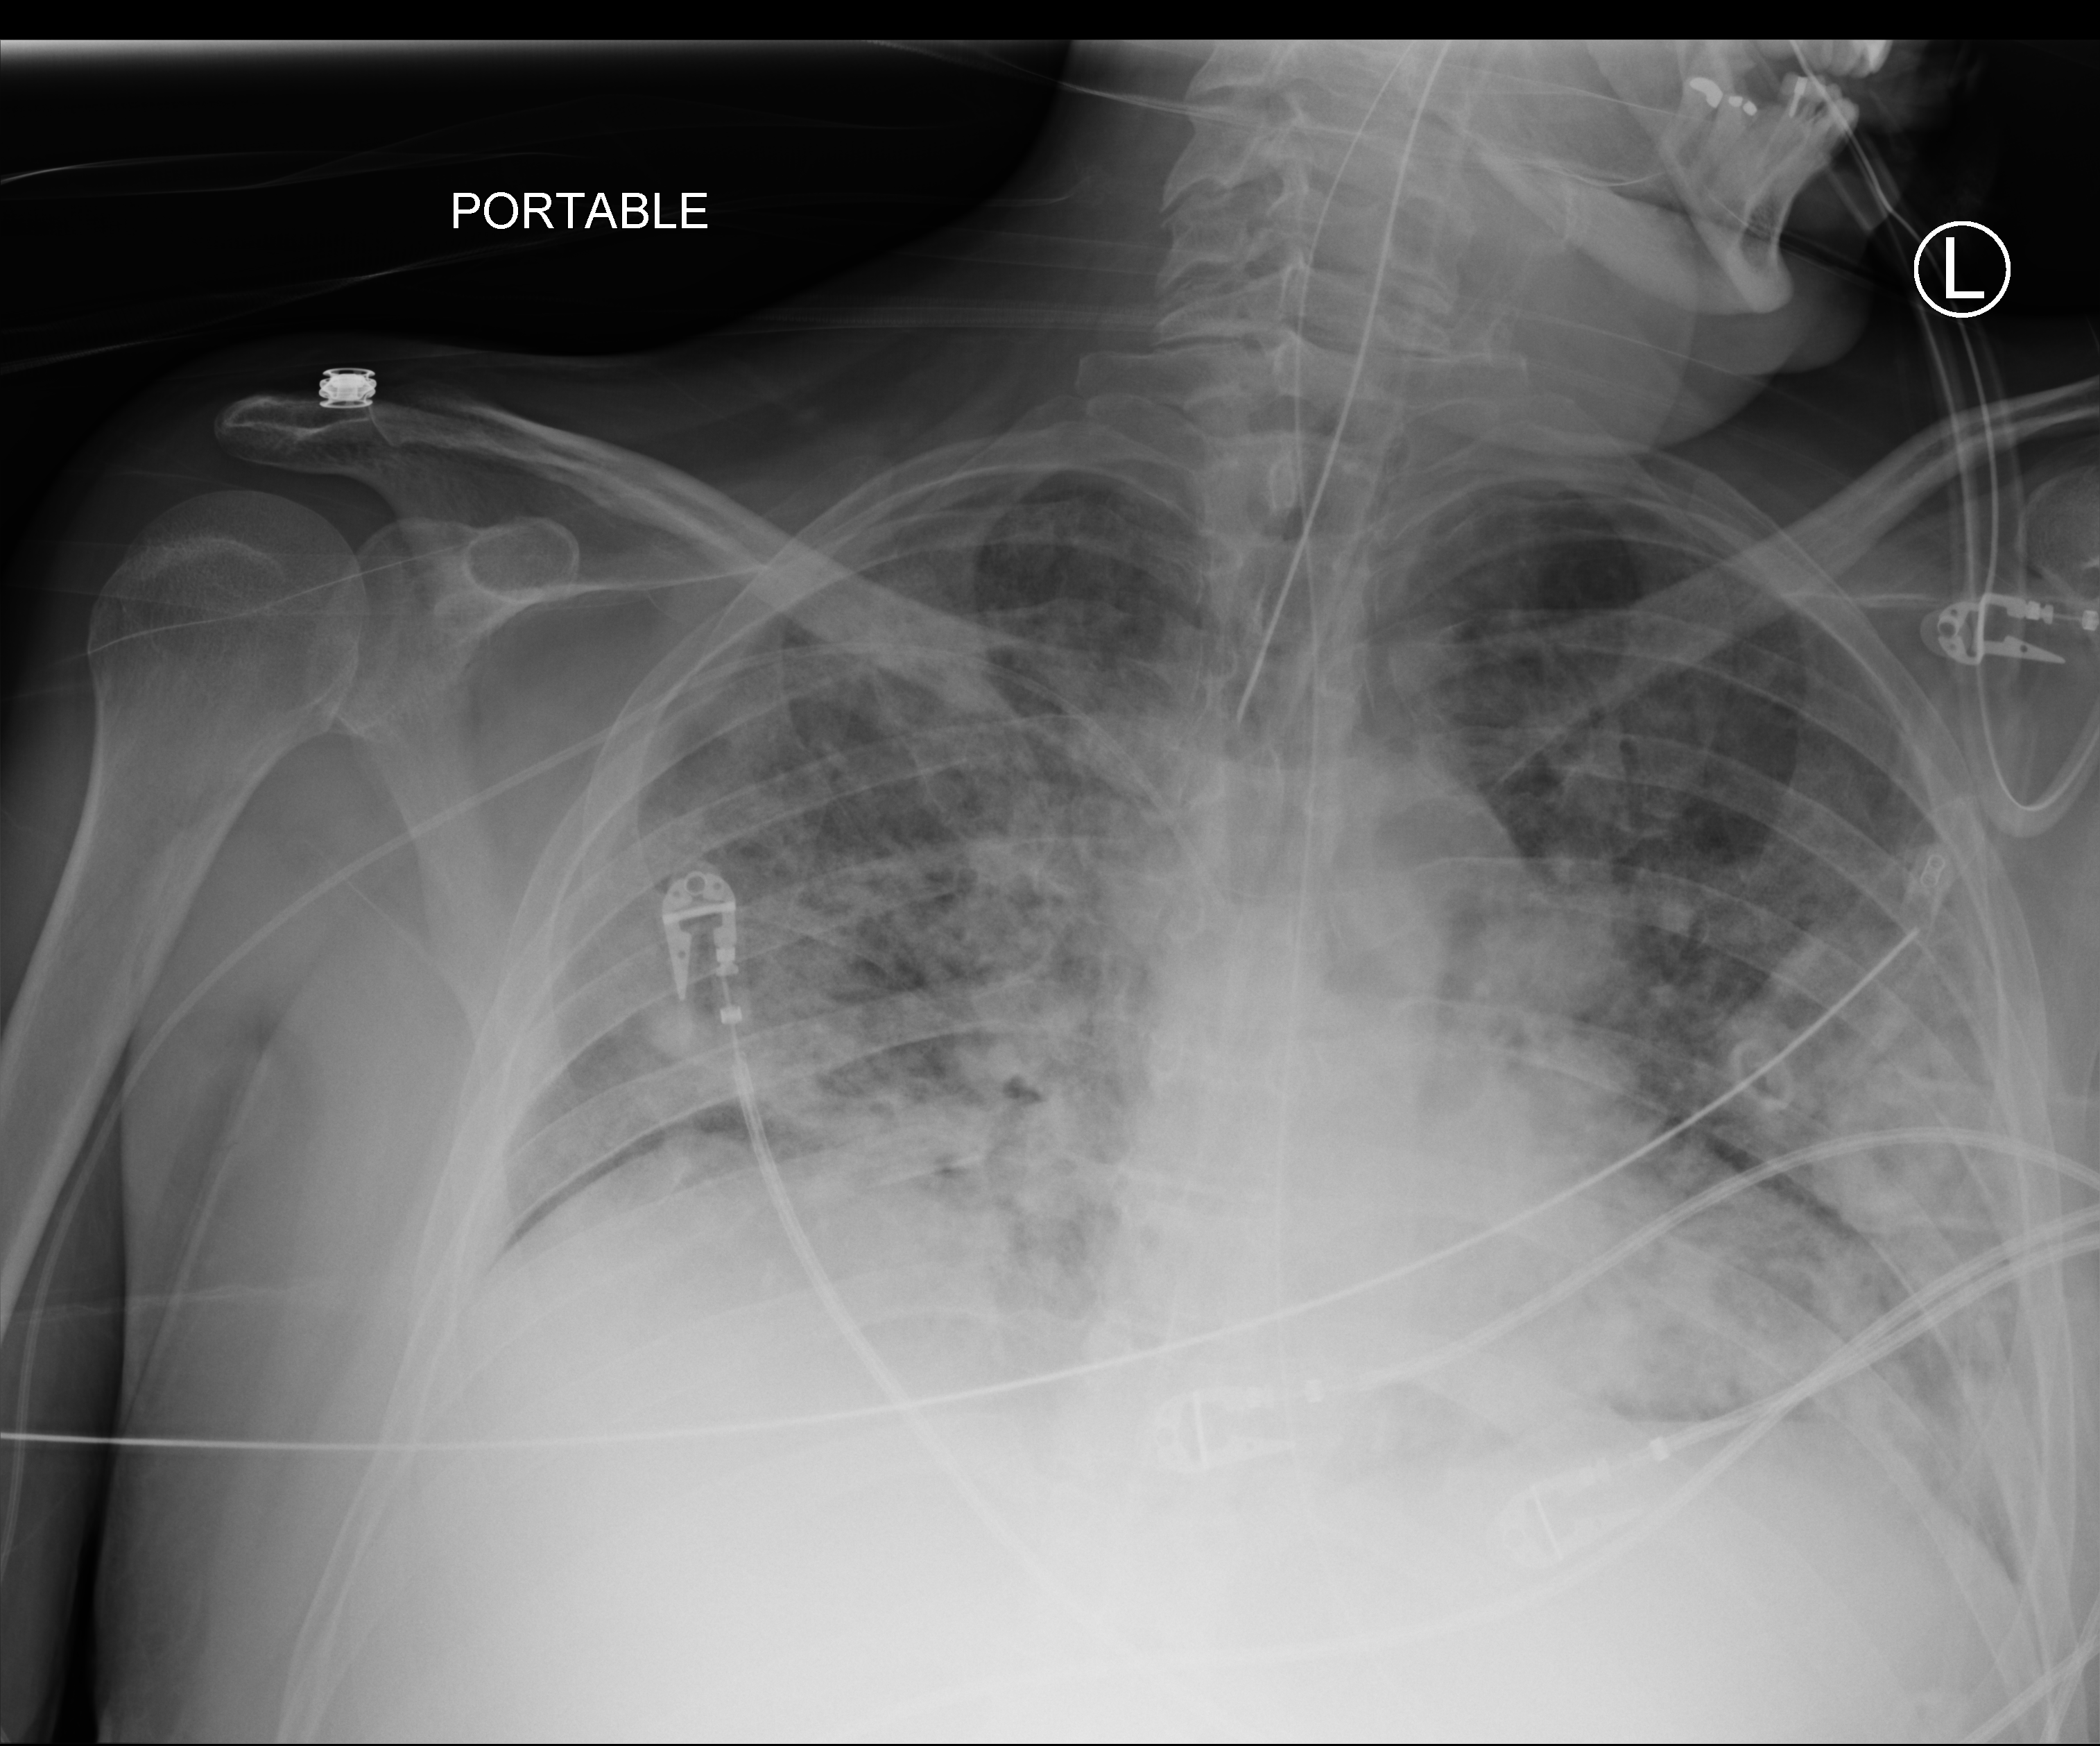
Chest X-ray (portable), anteroposterior (AP) projection. Male patient hospitalised with COVID-19, age 18–59 years.
From the hospital-stay record, not from the radiograph (when in the stay this image was taken is not recorded): admitted to intensive care during this hospital stay: yes.